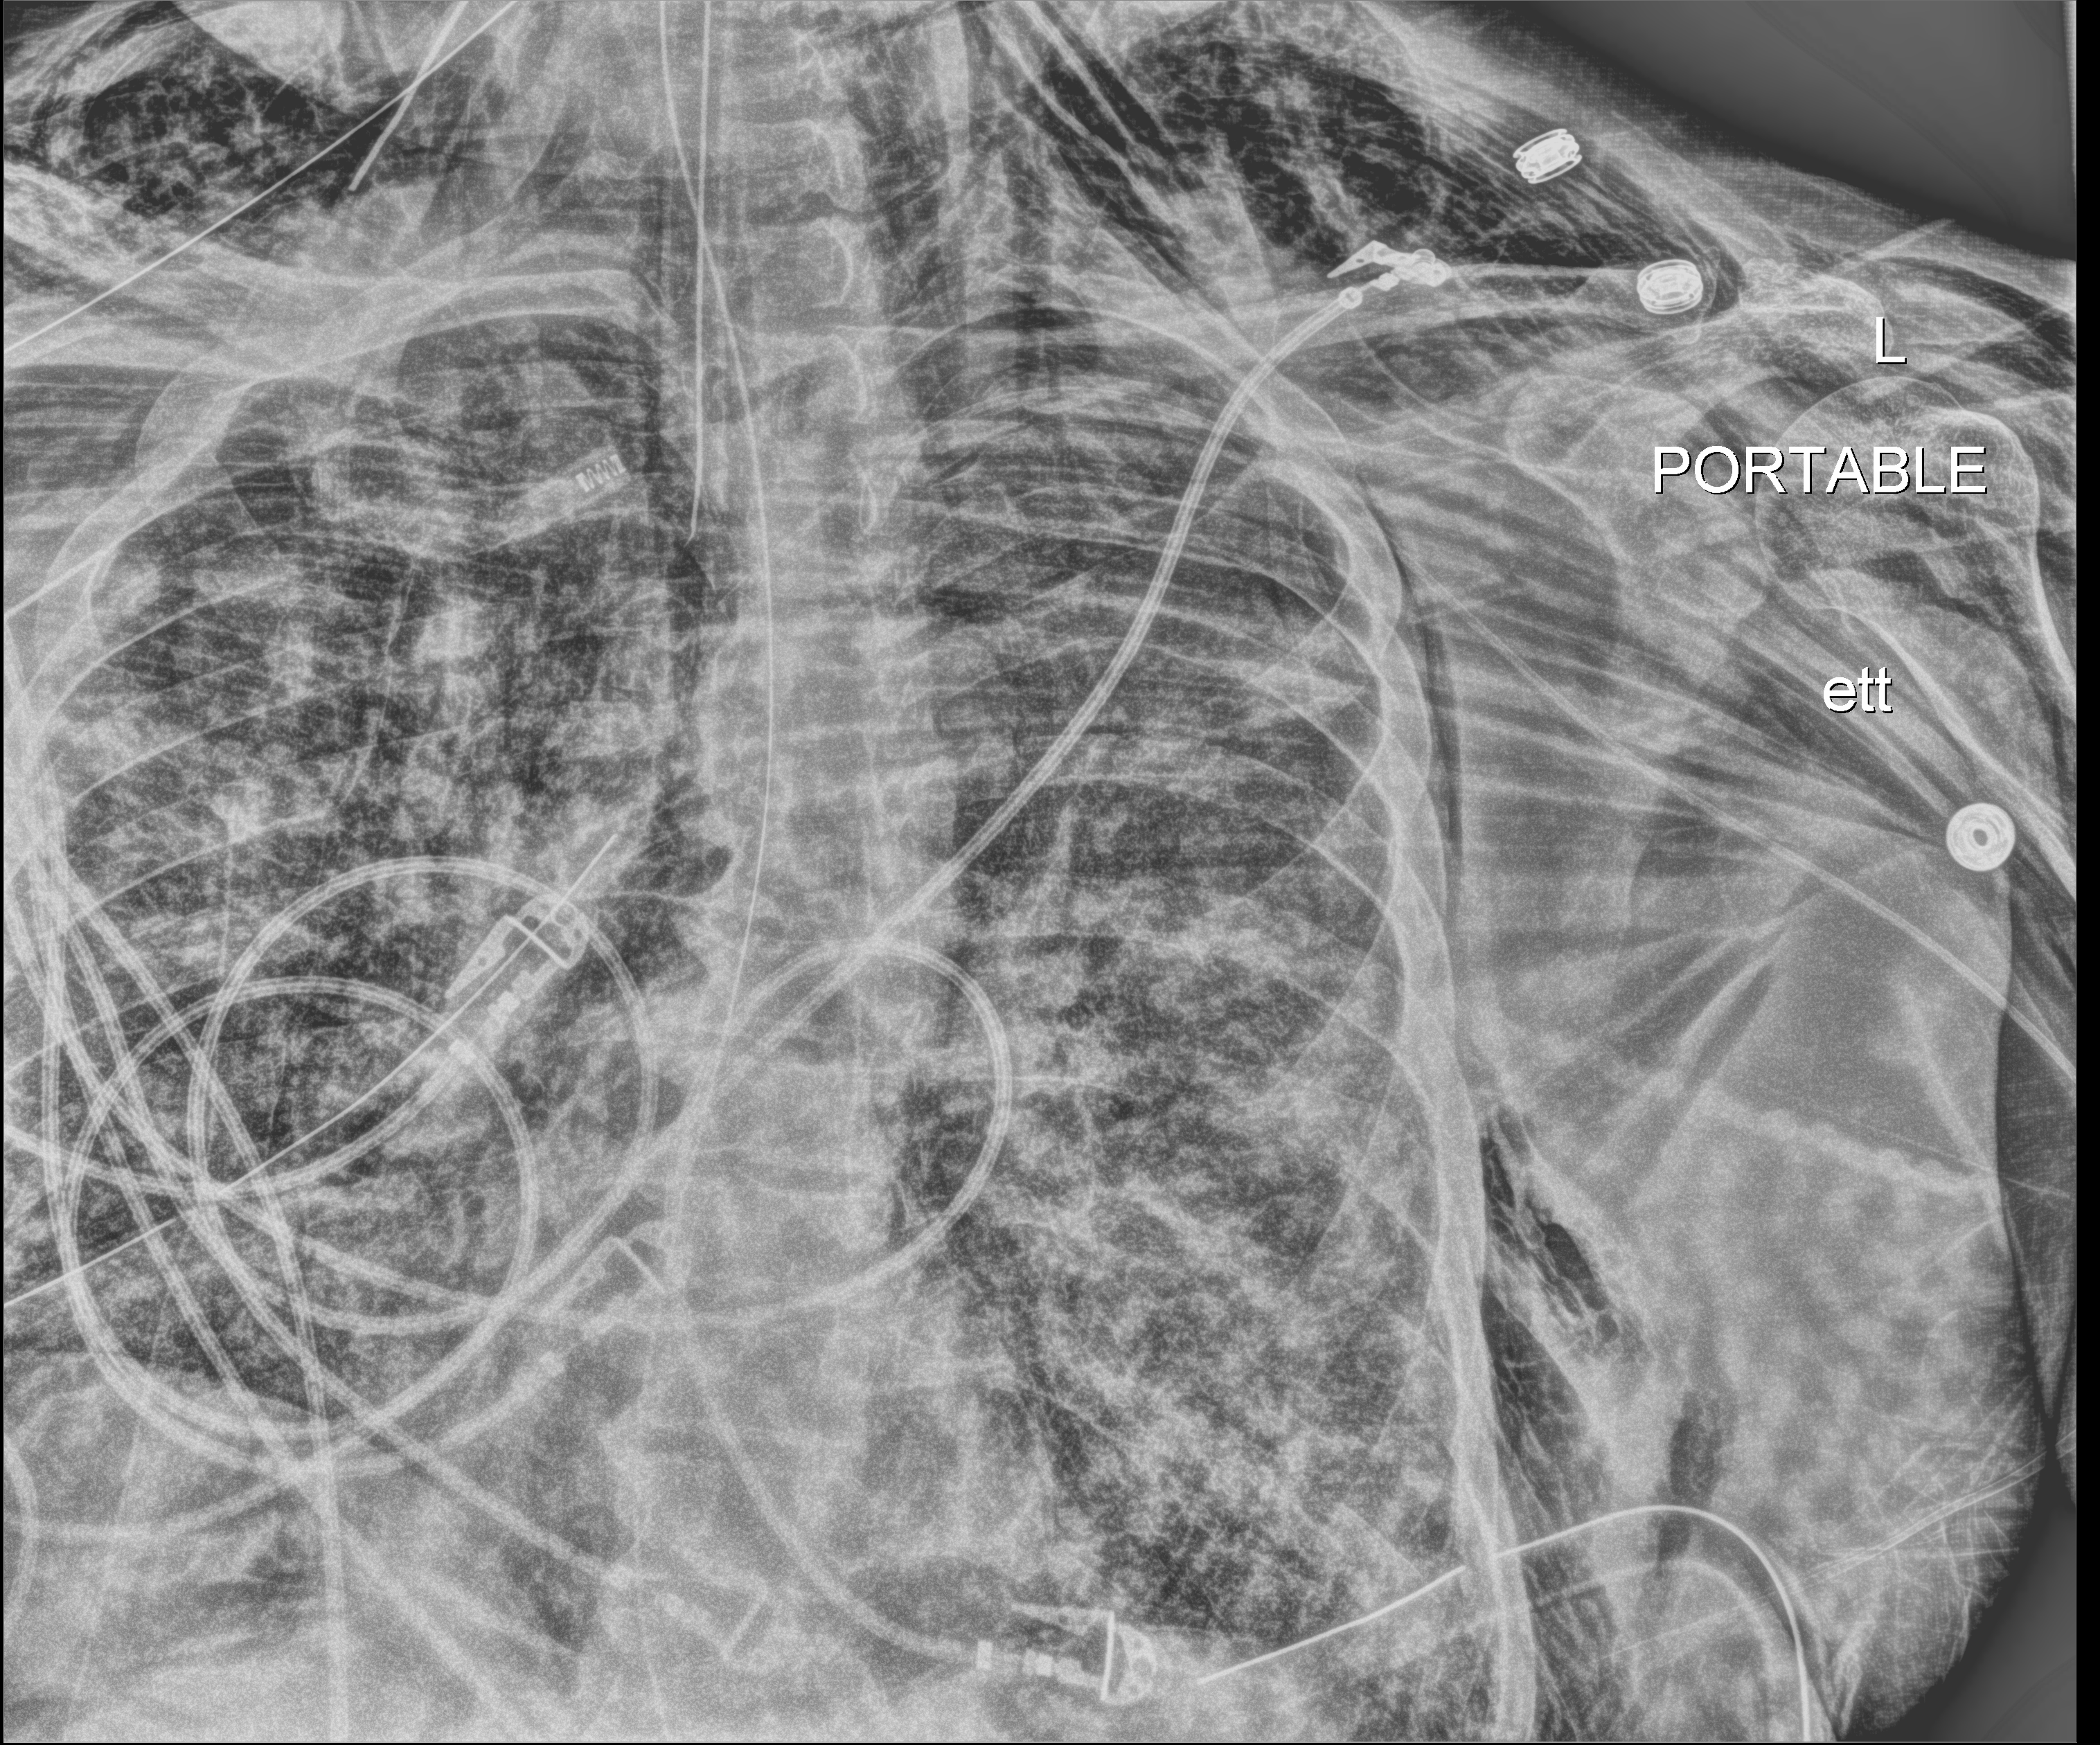
Bedside chest radiograph (digital radiography), anteroposterior (AP) projection. Adult patient hospitalised with COVID-19, age 18–59 years.
Admission-level facts for this patient (not findings on this image; timing relative to this image not recorded):
- length of hospital stay: 28 days
- chronic kidney disease (admission record): no